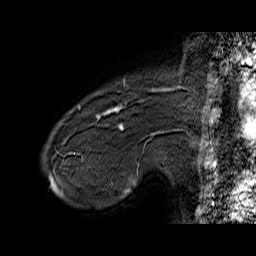
Breast MRI (dynamic contrast-enhanced), one sagittal slice. Position 10 of 60 along the scan axis. Dynamic contrast-enhanced series, time point 2 of 6 at this slice position (early post-contrast). 1.5 T. TE 6.4 ms, TR 32.9 ms. 256 × 256 image matrix, field of view 200 × 200 mm. Female patient. From the clinical record (not read from this slice): setting: breast cancer imaged before/during neoadjuvant chemotherapy; receptor status: HER2-positive.
Annotated regions visible in this slice (semi-automatically segmented with operator editing):
- analysis volume of interest (the breast-tissue region the enhancement analysis was run in; not a lesion): box from (x=71, y=80) to (x=155, y=146) px
- tumour enhancement mask (voxels above the 100 % enhancement threshold inside the analysis volume of interest): (x=97, y=106)–(x=123, y=127)